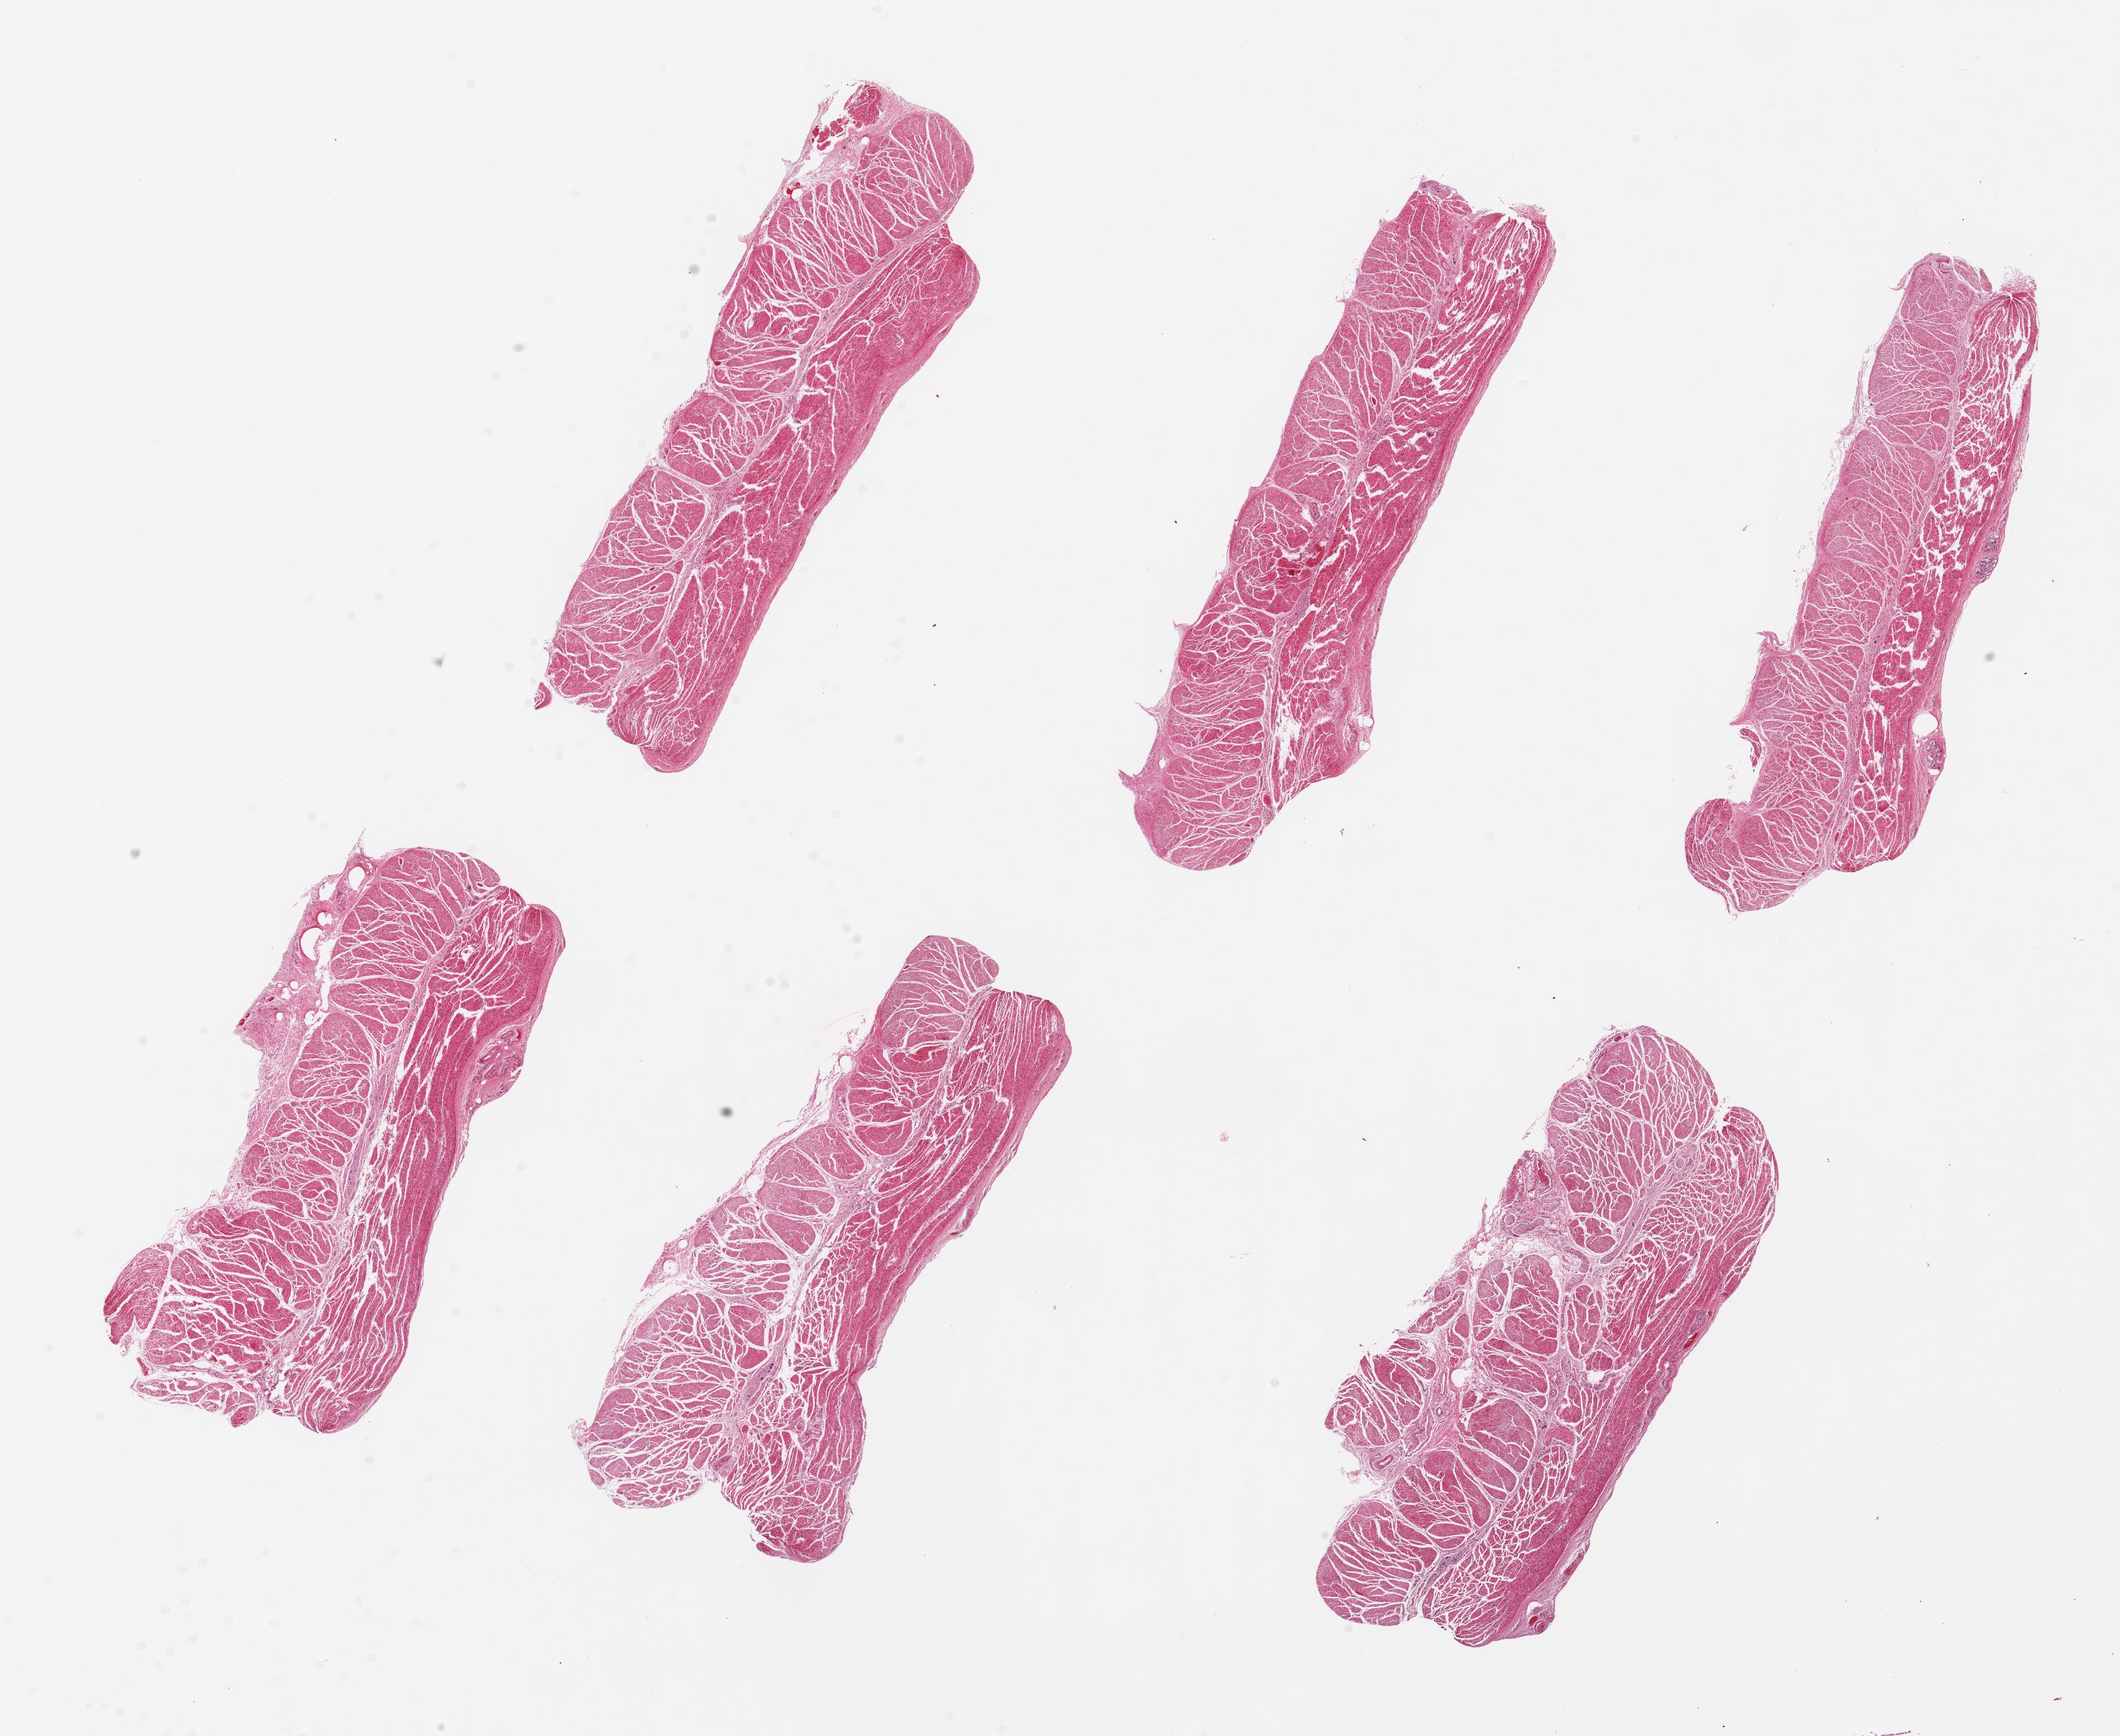
H&E whole-slide image, brightfield, shown as a low-resolution overview of the whole scanned area (about 23.6 x 19.3 mm, from a 20x scan); PAXgene-fixed paraffin-embedded (PFPE) section; target tissue: esophageal muscle; donor tissue sample. Donor: male.
- pathologist's review note for this sample: 6 pieces up to 8x3mm; more poorly preserved than usual